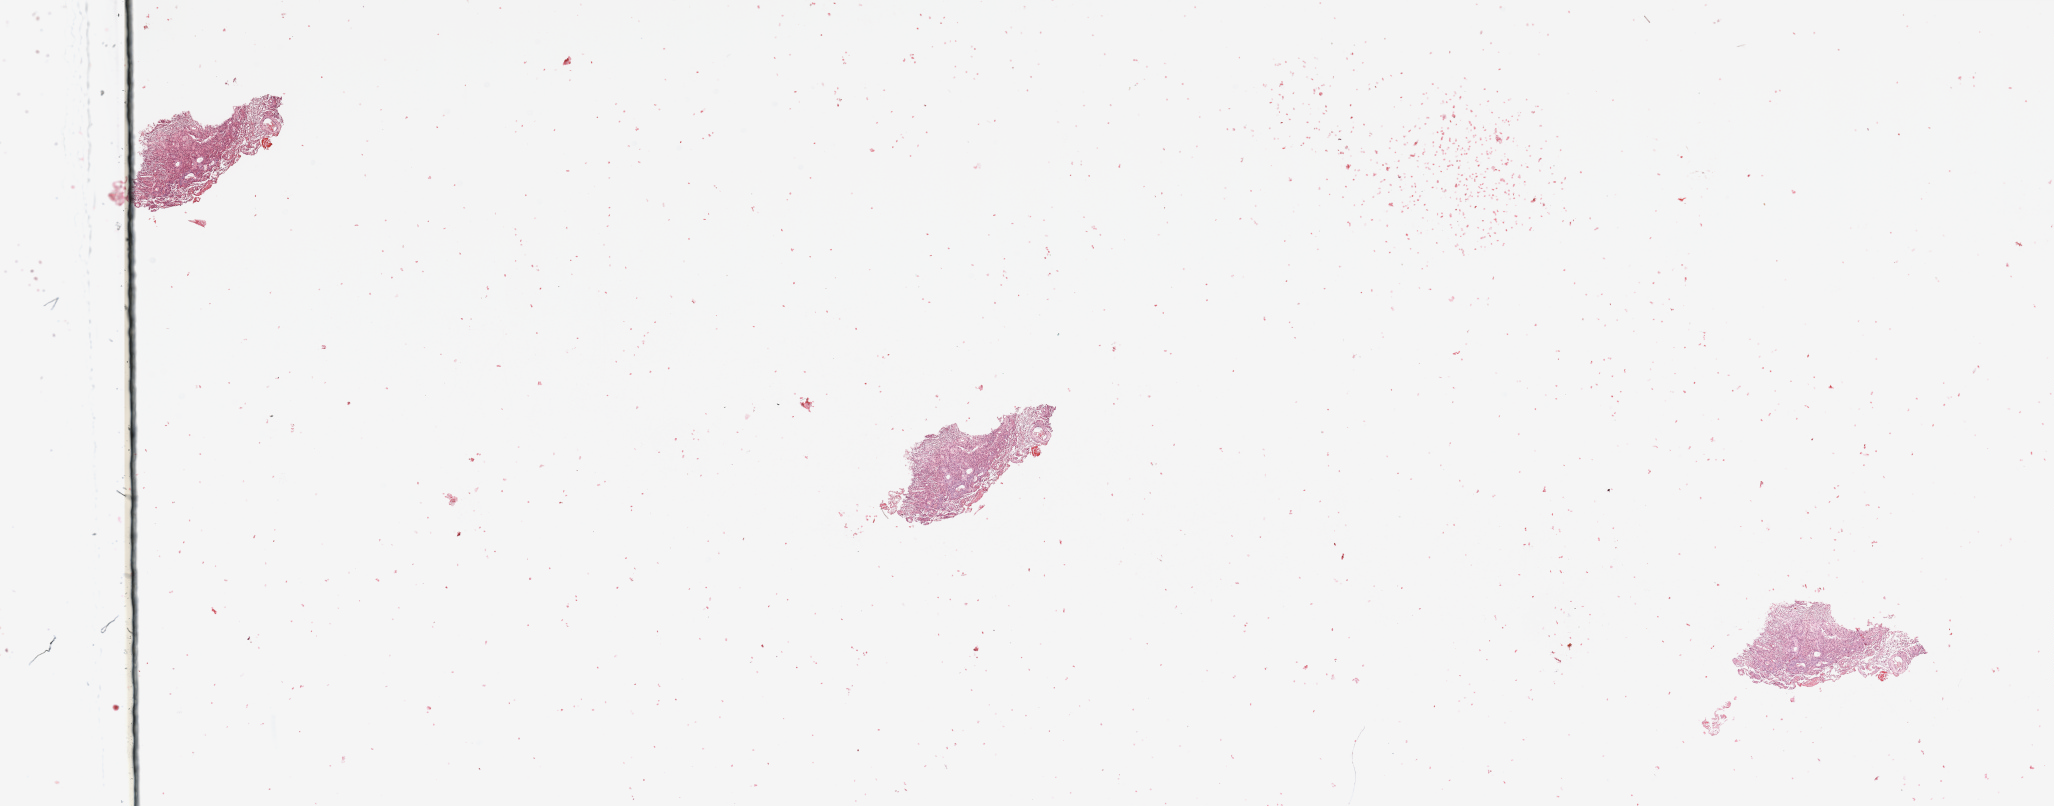
Digitized H&E-stained tissue section (whole slide), low-resolution overview of the scanned area, about 32.5 x 12.7 mm (slide scanned at 20x). Tumour tissue sample, sampled site: frontal lobe. Male, 62 y/o. Composition of this section per pathologist review: tumour nuclei 75%, necrosis 0%.
- histologic diagnosis: Glioblastoma
- primary tumour site (as recorded): frontal lobe